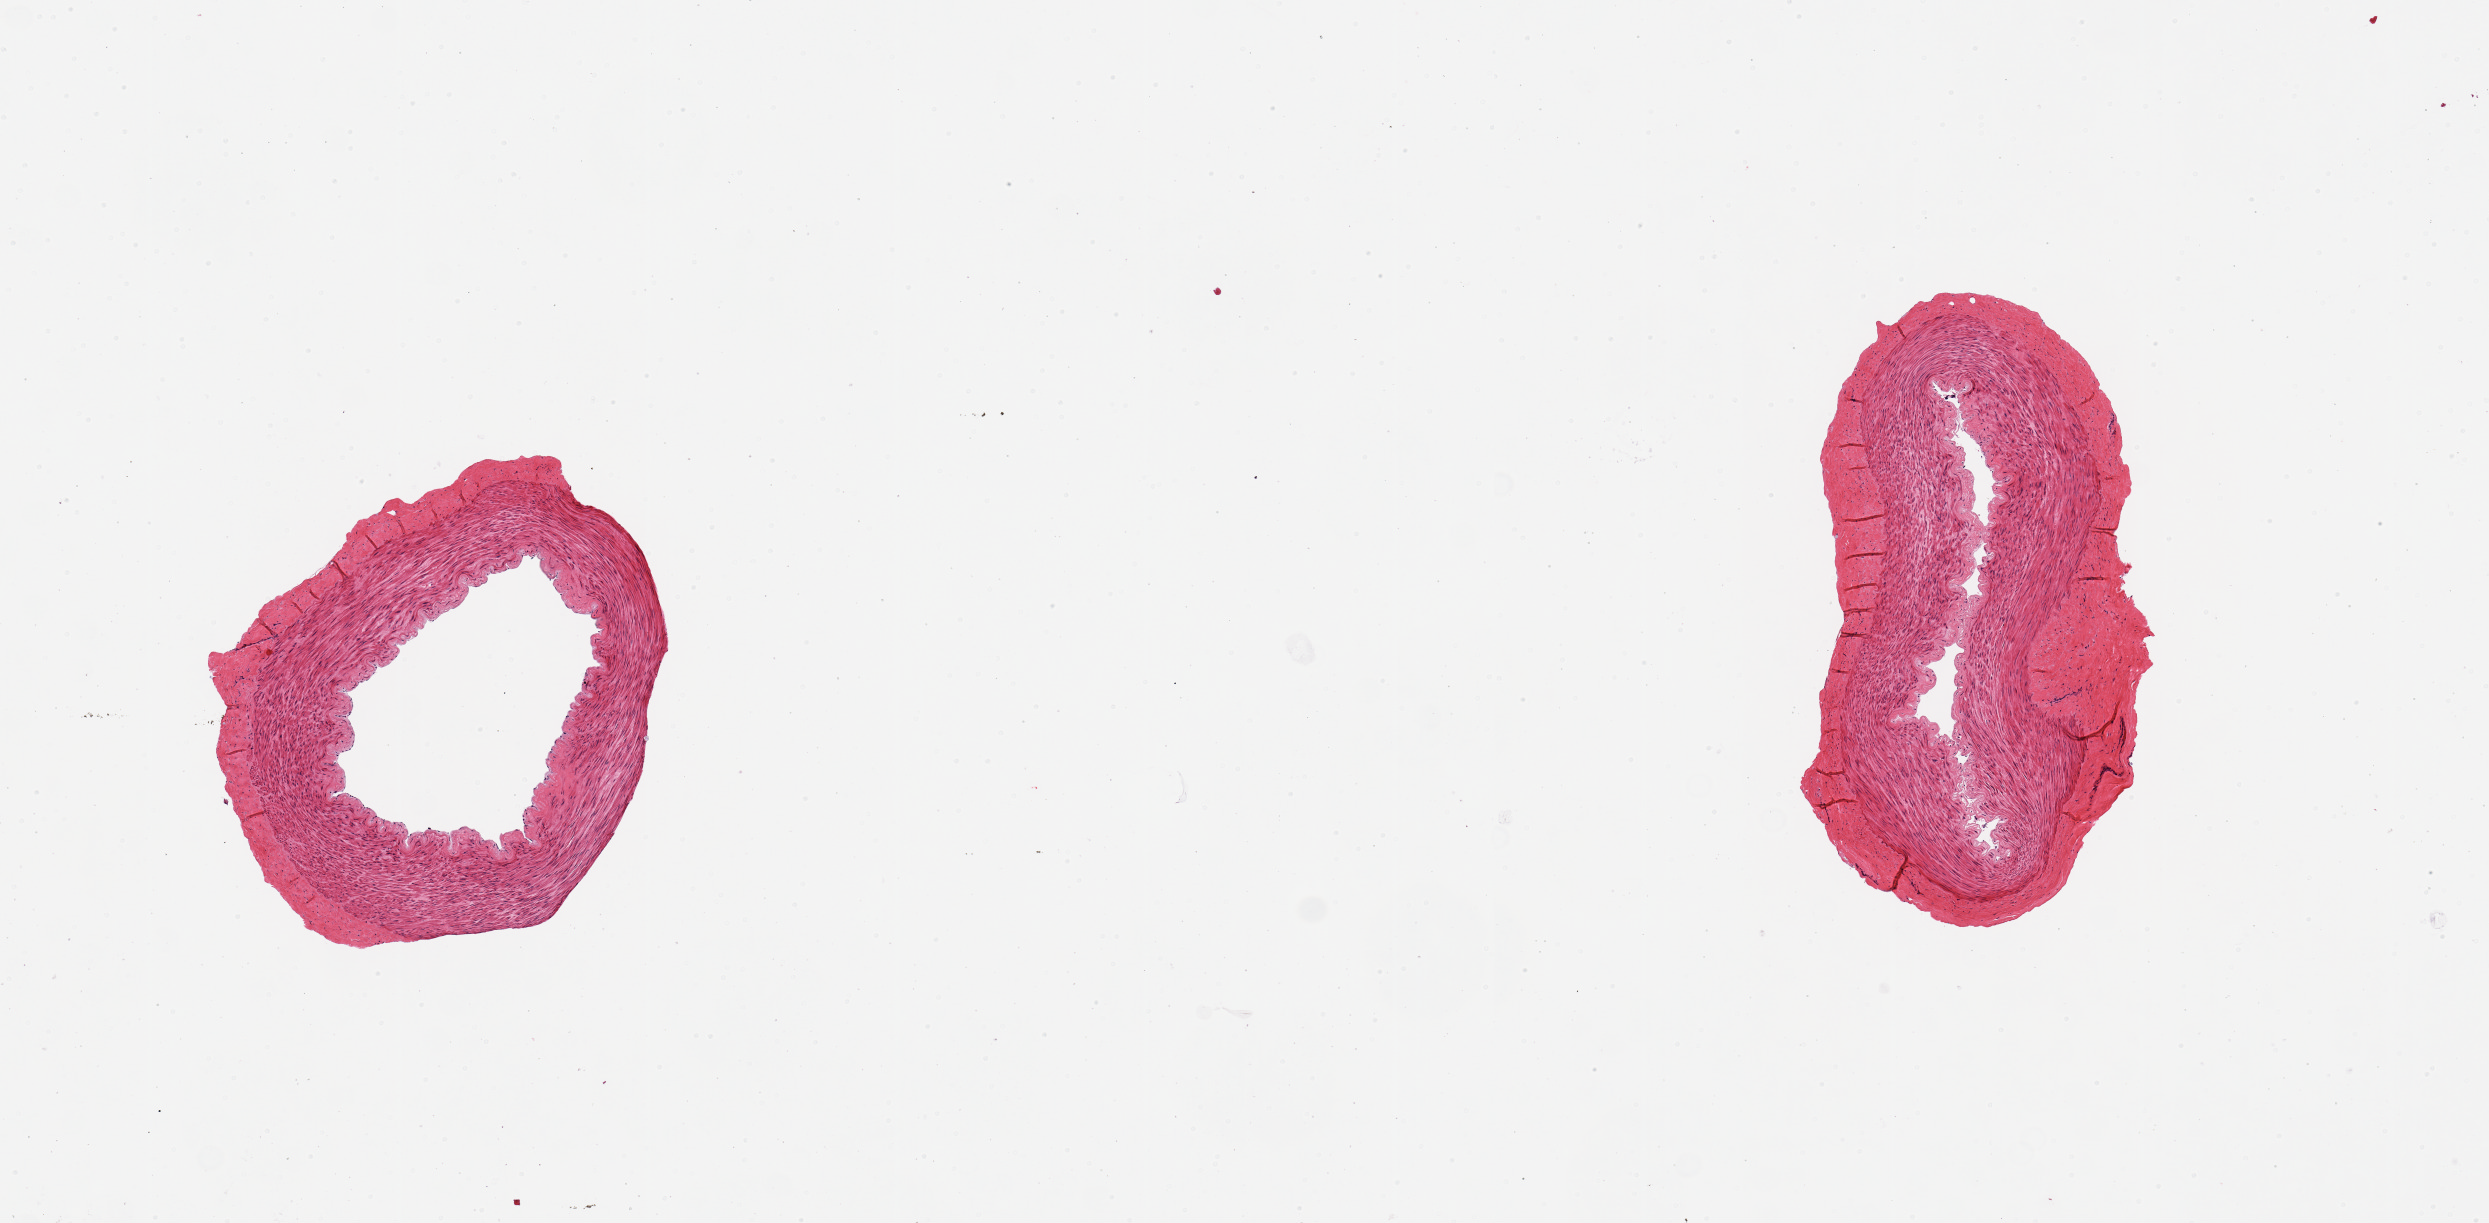
H&E whole-slide image, brightfield, low-resolution overview of the scanned area, about 9.8 x 4.8 mm (slide scanned at 20x), PAXgene-fixed paraffin-embedded (PFPE) section, target tissue: tibial artery, tissue donor sample. Donor sex: female.
* reviewer comment on this tissue sample: 2 pieces, well trimmed